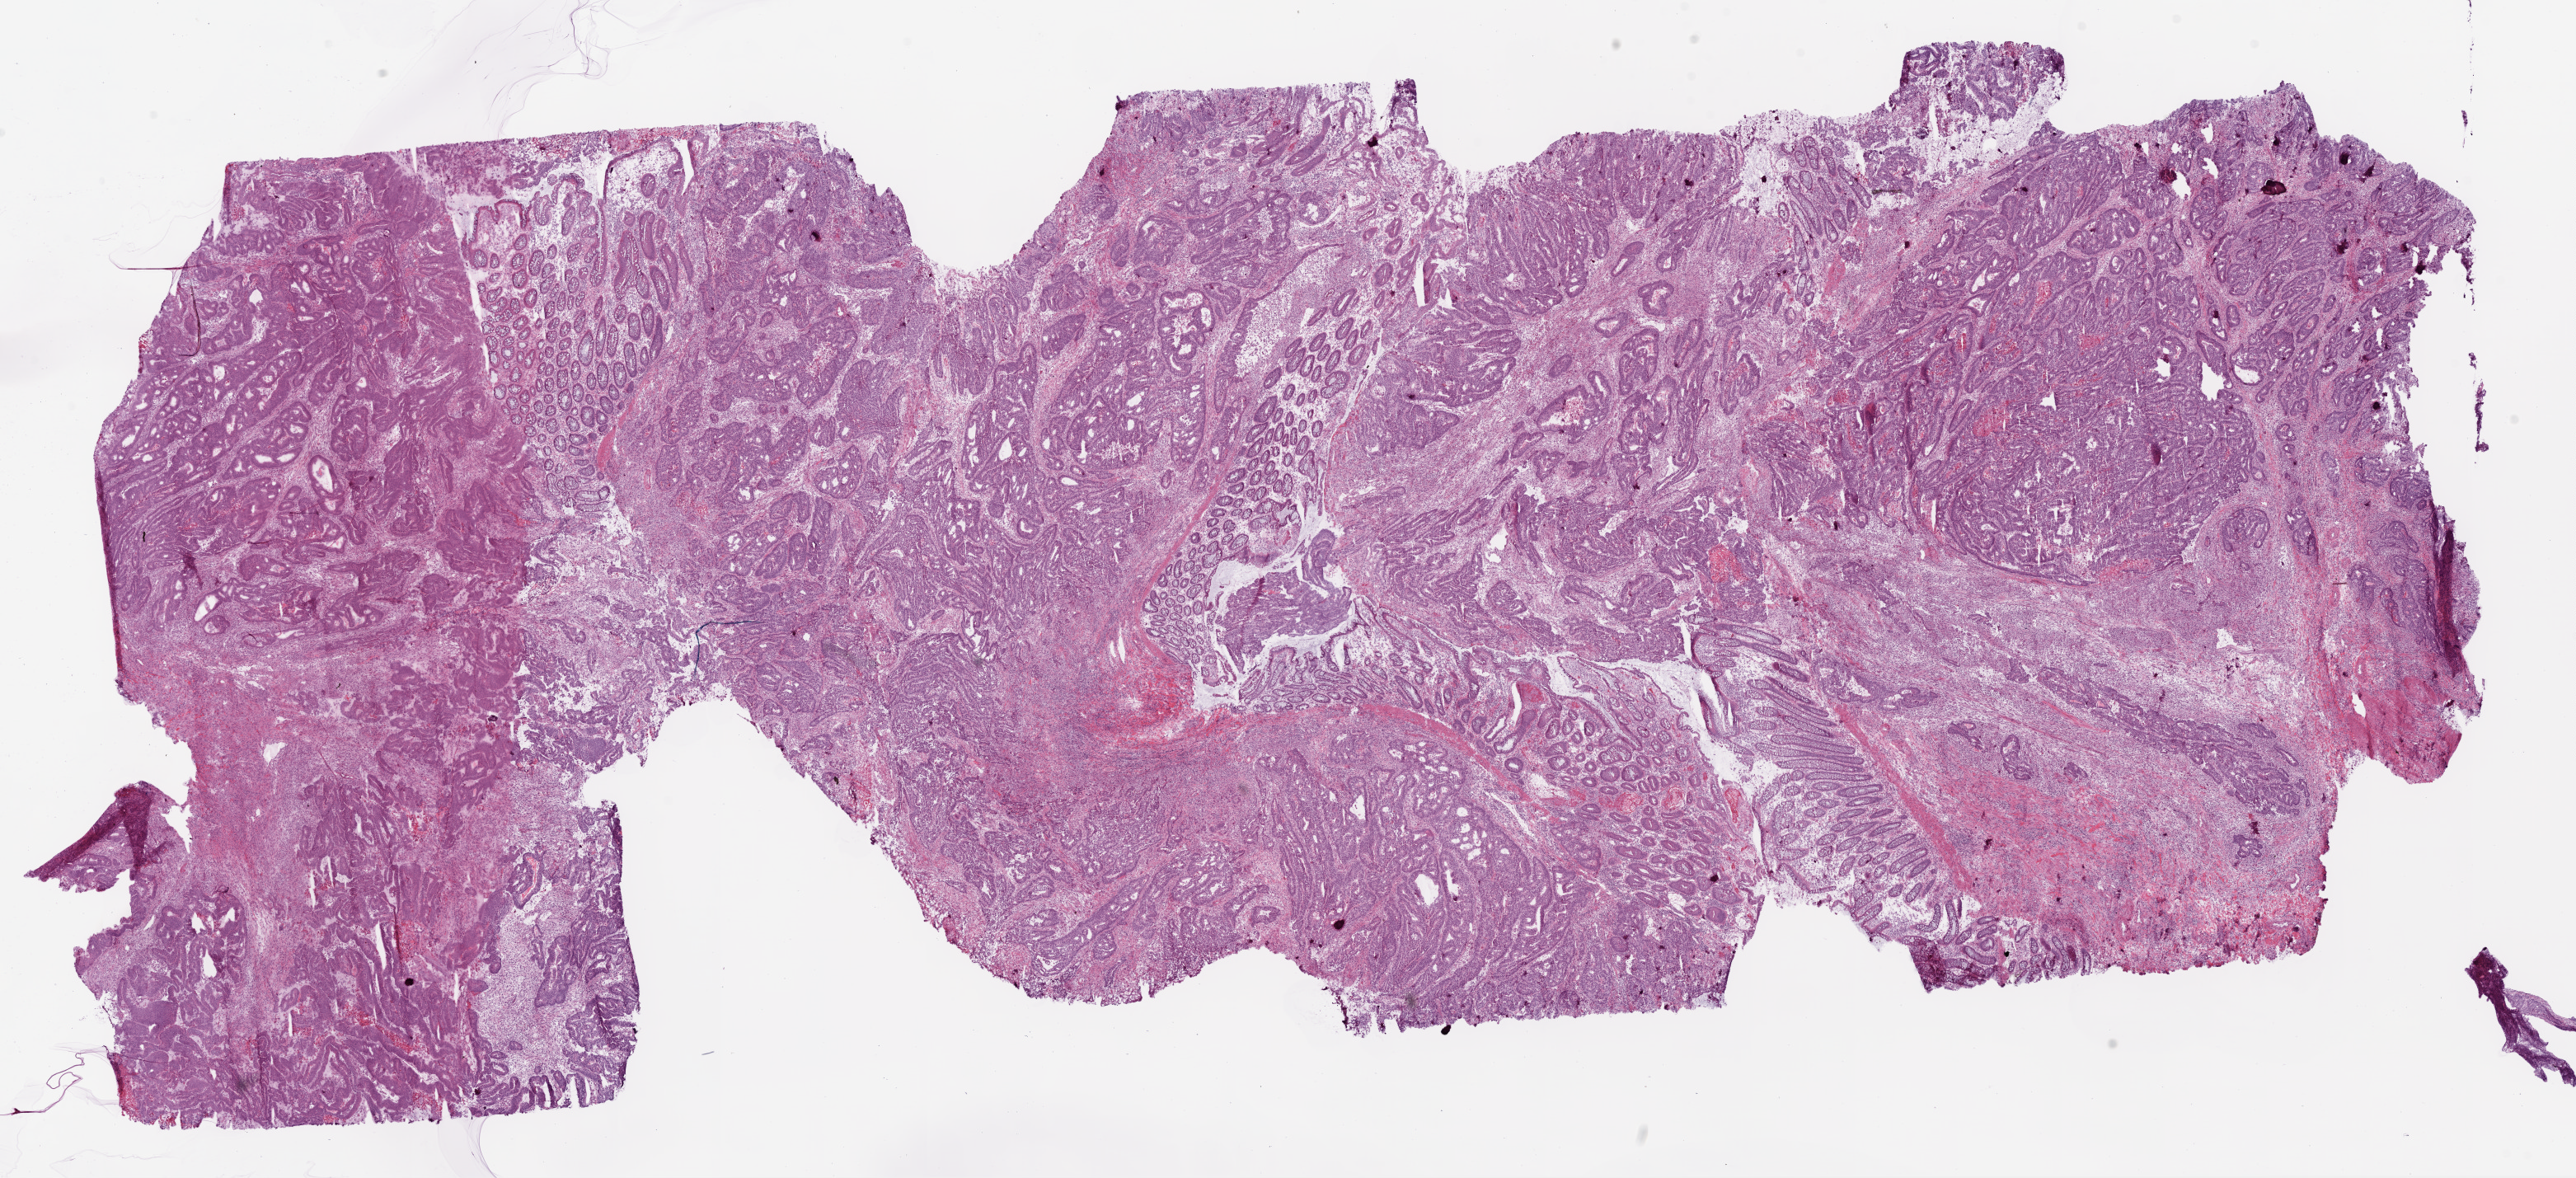
Digitized H&E-stained tissue section (whole slide) — a low-resolution overview of the entire scanned area, about 25.1 x 11.5 mm, frozen section, colon, primary tumour sample. Male, age 79 years at initial diagnosis. Slide review estimates, as recorded: tumour cells 60%, tumour nuclei 70%, normal cells 20%, stromal cells 10%, necrosis 10%.
Pathologic diagnosis: Adenocarcinoma, NOS. Lymph nodes positive (case pathology): 0 of 19 examined. AJCC pathologic stage: IIA (7th edition).